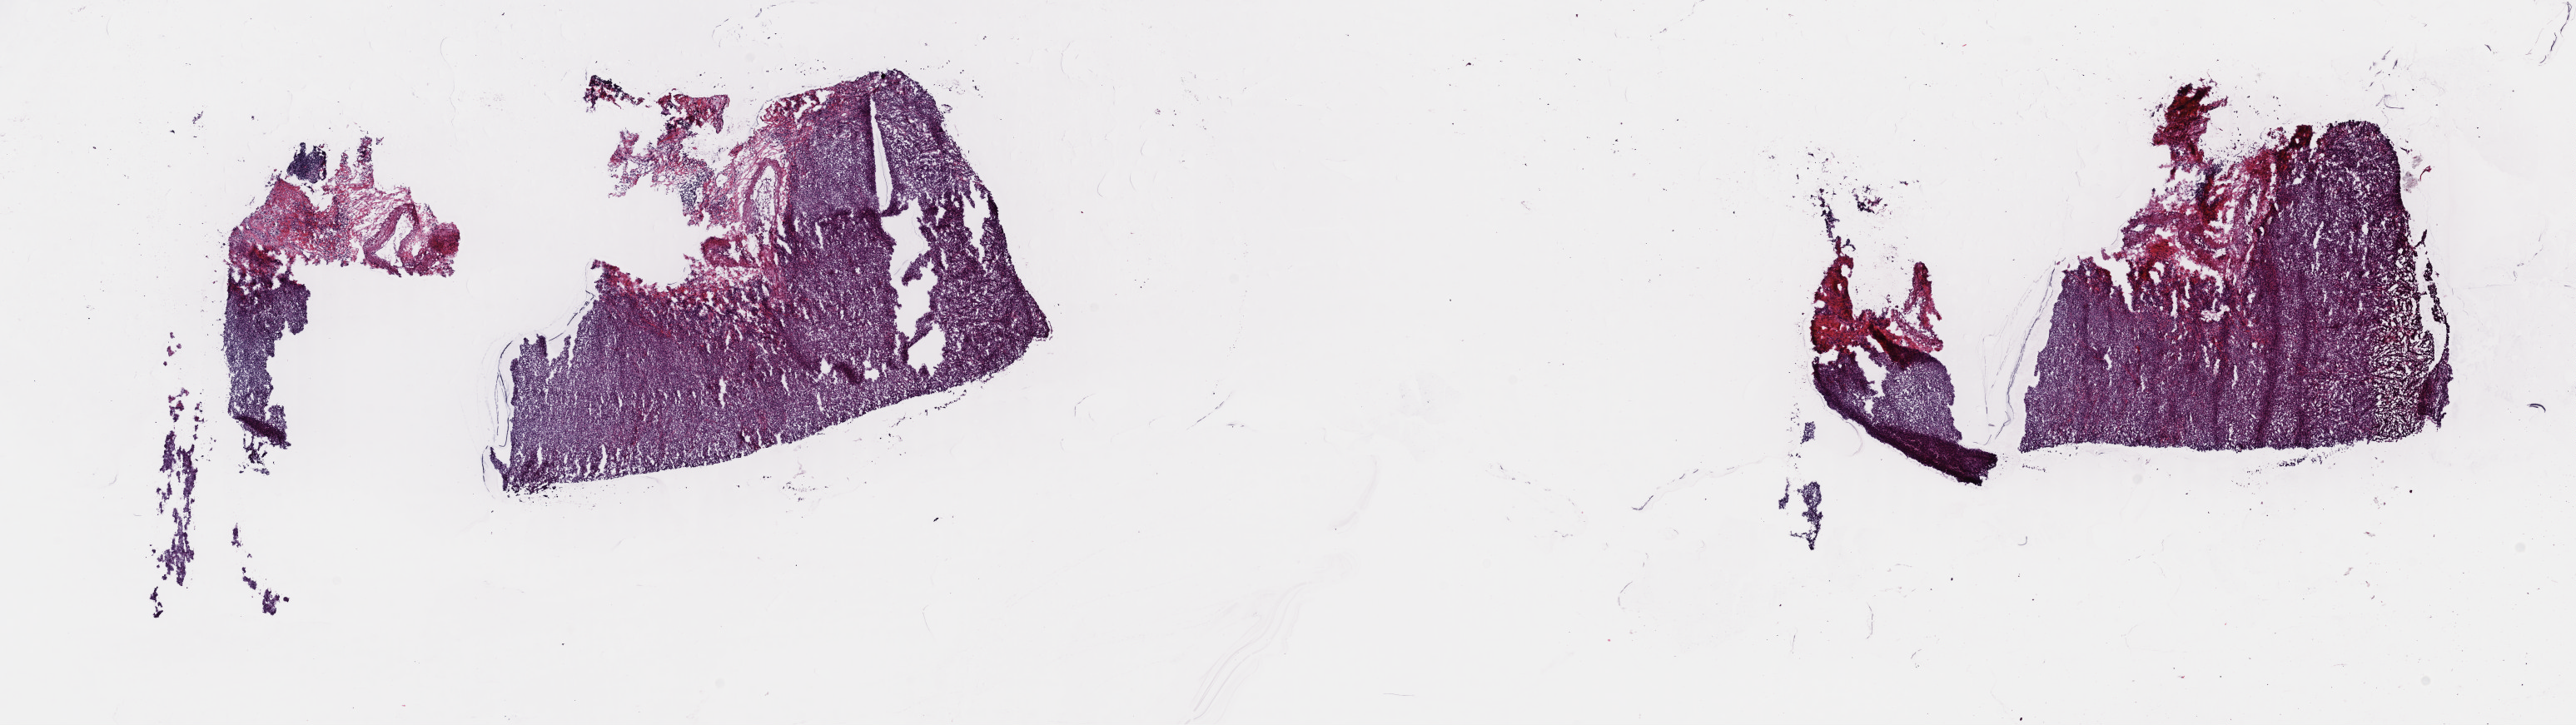
Digitized Hematoxylin and eosin (H&E) stained tissue section (whole slide) — a low-resolution overview of the entire scanned area, about 24.4 x 6.9 mm. Frozen section. Primary tumour sample from the bladder. Male, age 75 years at initial diagnosis. Histologic grade: high grade. Slide review estimates, as recorded: tumour cells 70%, tumour nuclei 75%, normal cells 0%, stromal cells 25%, necrosis 5%. Inflammatory infiltration, as recorded: lymphocyte infiltration 5%, monocyte infiltration 0%, neutrophil infiltration 0%.
• lymph nodes positive (case pathology): 0 of 13 examined
• AJCC pathologic stage: III (6th edition)
• histologic diagnosis: Transitional cell carcinoma (lateral wall of bladder)